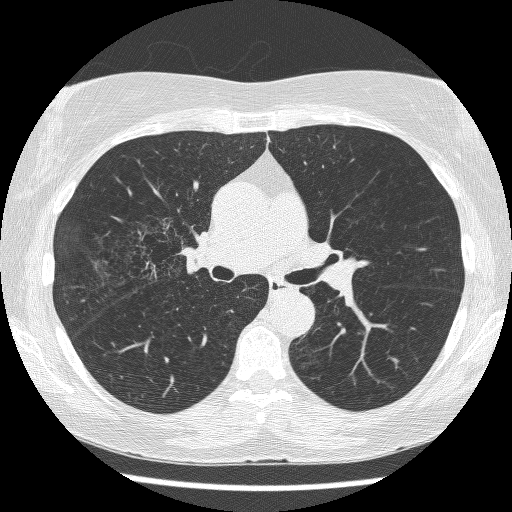
Chest CT (low-dose screening protocol), one axial image, baseline screening round, lung window (W 1500 / L -600 HU), lung (sharp) reconstruction kernel (BONE), slice 166 of 271 in the series. Female participant, aged 64 years at enrolment.
Lesion marked by an expert reader, box from (x=123, y=215) to (x=200, y=277) px. The screening reader recorded 3 non-calcified nodules or masses ≥4 mm on this exam (right upper lobe, right upper lobe, left lower lobe); which of them this box marks is not recorded.